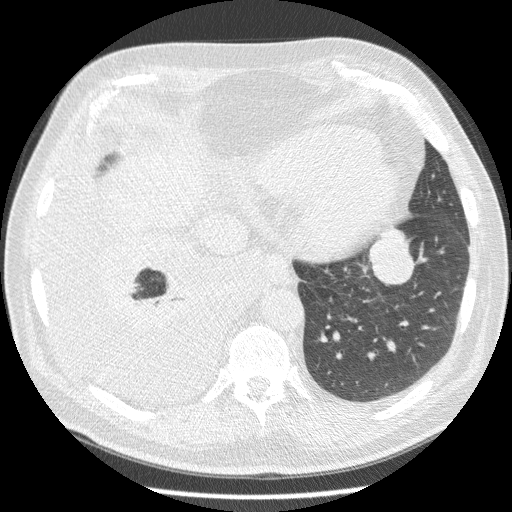
Chest CT (low-dose screening protocol), one axial image. Third annual screen. Lung window (W 1500 / L -600 HU). 2.5 mm slice thickness. Standard (soft-tissue) reconstruction kernel (STANDARD). Slice 56 of 180 in the series. Male participant, aged 63 years at enrolment. Current smoker at enrolment.
Lesion marked by an expert reader, bounding box <355,220,420,287> (left, top, right, bottom; pixels). Screening reader's record for this exam (one nodule recorded; not confirmed to be the boxed lesion): non-calcified nodule or mass ≥4 mm, left lower lobe, 34 × 31 mm, smooth margins, soft tissue attenuation, pre-existing on the prior screen: yes; interval growth: yes. Official screen result: positive, other. Participant outcome: lung cancer diagnosed 30 days after this screen — squamous cell carcinoma, NOS, left lower lobe, stage IB (AJCC 6th edition), 48 mm at pathology.